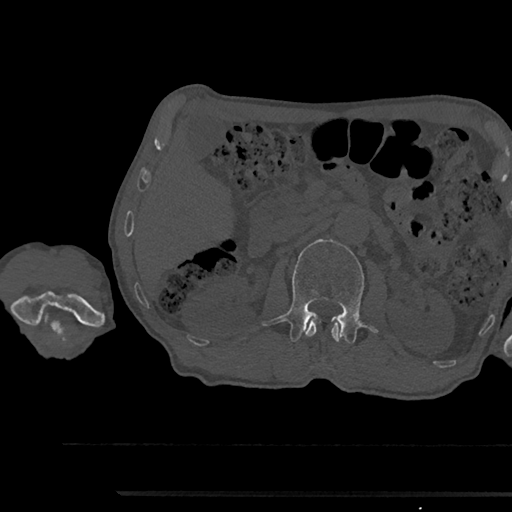
CT including the spine, one axial slice. Slice 588 of 797 in the series (ordered by position). Reconstruction kernel Br40s/3. Bone window (W 1800 / L 400 HU). 0.5 mm slice thickness. 512 × 512 image matrix. Male patient, age 79 years. Case-level facts recorded for this patient, not image findings: primary cancer: prostate.
Structures marked on this image (semi-automatic segmentation, software-assisted and operator-edited):
- L1 vertebra: bounding box (x1, y1, x2, y2) in pixels: (305, 319, 341, 342)
- L2 vertebra: (262, 239, 377, 343)